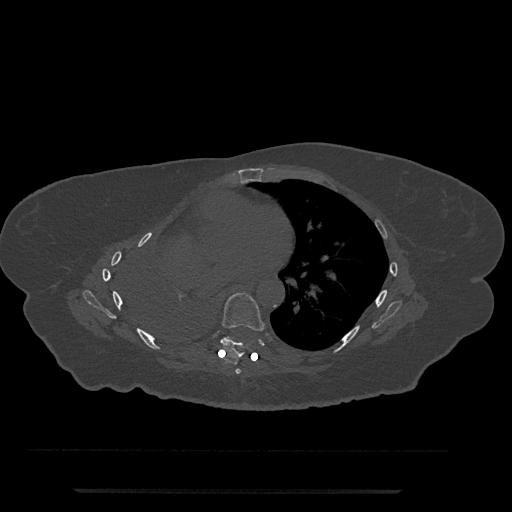
CT including the spine, one axial slice. Position 436 of 797 along the scan axis. Bone window (W 1800 / L 400 HU). 512 × 512 image matrix, field of view 440 × 440 mm. Female patient, age 51 years. From the clinical record (not read from this slice): primary cancer: neuro.
Outlined on this slice (semi-automatically segmented with operator editing):
- T6 vertebra: bounding box (x1, y1, x2, y2) in pixels: (235, 369, 241, 374)
- T7 vertebra: (220, 293, 265, 358)
- T8 vertebra: (224, 337, 229, 339)